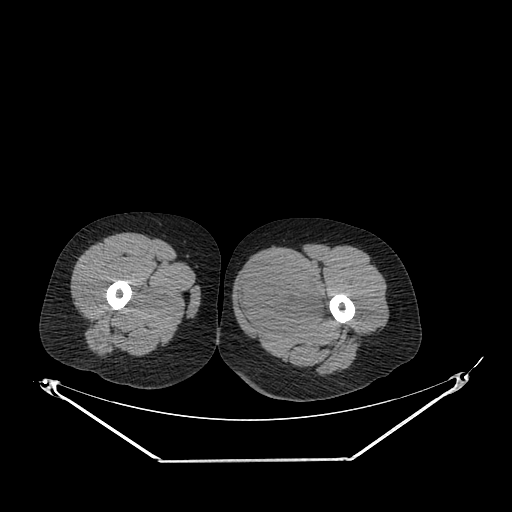
CT of an extremity soft-tissue mass (from a PET/CT study), one axial slice; slice 237 of 267 in the series (ordered by position); reconstruction kernel SOFT; 120 kVp; soft-tissue window (W 400 / L 40 HU); 3.75 mm slice thickness; 512 × 512 image matrix, field of view 500 × 500 mm. Female patient. Case-level facts recorded for this patient, not image findings: histological type: pleiomorphic leiomyosarcoma; grade: intermediate; site of the primary tumour: left thigh.
Outlined on this slice (expert contour drawn on MRI and transferred to this co-registered scan by the dataset authors):
- gross tumour volume including surrounding oedema: box from (x=237, y=258) to (x=330, y=332) px
- gross tumour volume (mass): (x=237, y=260)–(x=328, y=330)